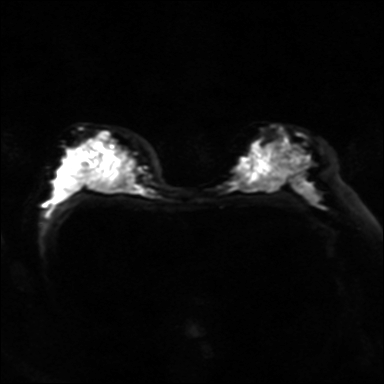
Breast MRI, one axial slice; slice 23 of 40 in the series (ordered by position); diffusion-weighted series; image 2 of 4 stored at this slice position (different b-values; order by instance number); 3 T; 4 mm slice thickness; 384 × 384 image matrix. Female patient.
Annotated regions visible in this slice (expert manual segmentation):
- tumour on diffusion-weighted imaging: bounding box [x1, y1, x2, y2] px = [96, 132, 109, 148]